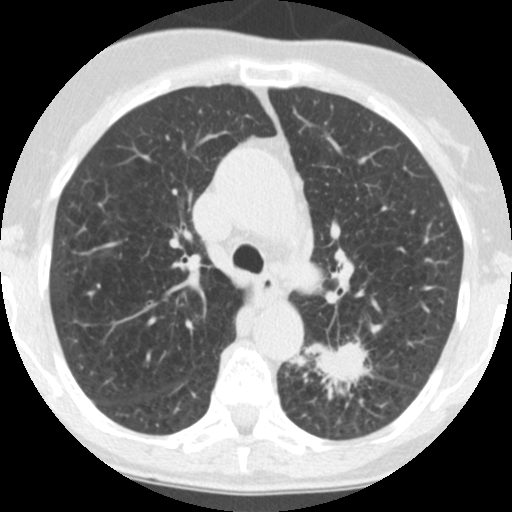
Chest CT (low-dose screening protocol), one axial image. Third screening round (two years after baseline). Lung window (W 1500 / L -600 HU). 2.5 mm slice thickness. Standard (soft-tissue) reconstruction kernel (STANDARD). Female participant, aged 71 years at enrolment. Current smoker at enrolment.
Lesion marked by an expert reader, bounding box (x1, y1, x2, y2) in pixels: (297, 332, 380, 411). The screening reader recorded 2 non-calcified nodules or masses ≥4 mm on this exam (left lower lobe, left lower lobe); which of them this box marks is not recorded. Participant outcome: lung cancer diagnosed 26 days after this screen — squamous cell carcinoma, NOS, left lower lobe, poorly differentiated (G3), stage IB (AJCC 6th edition), 40 mm at pathology.